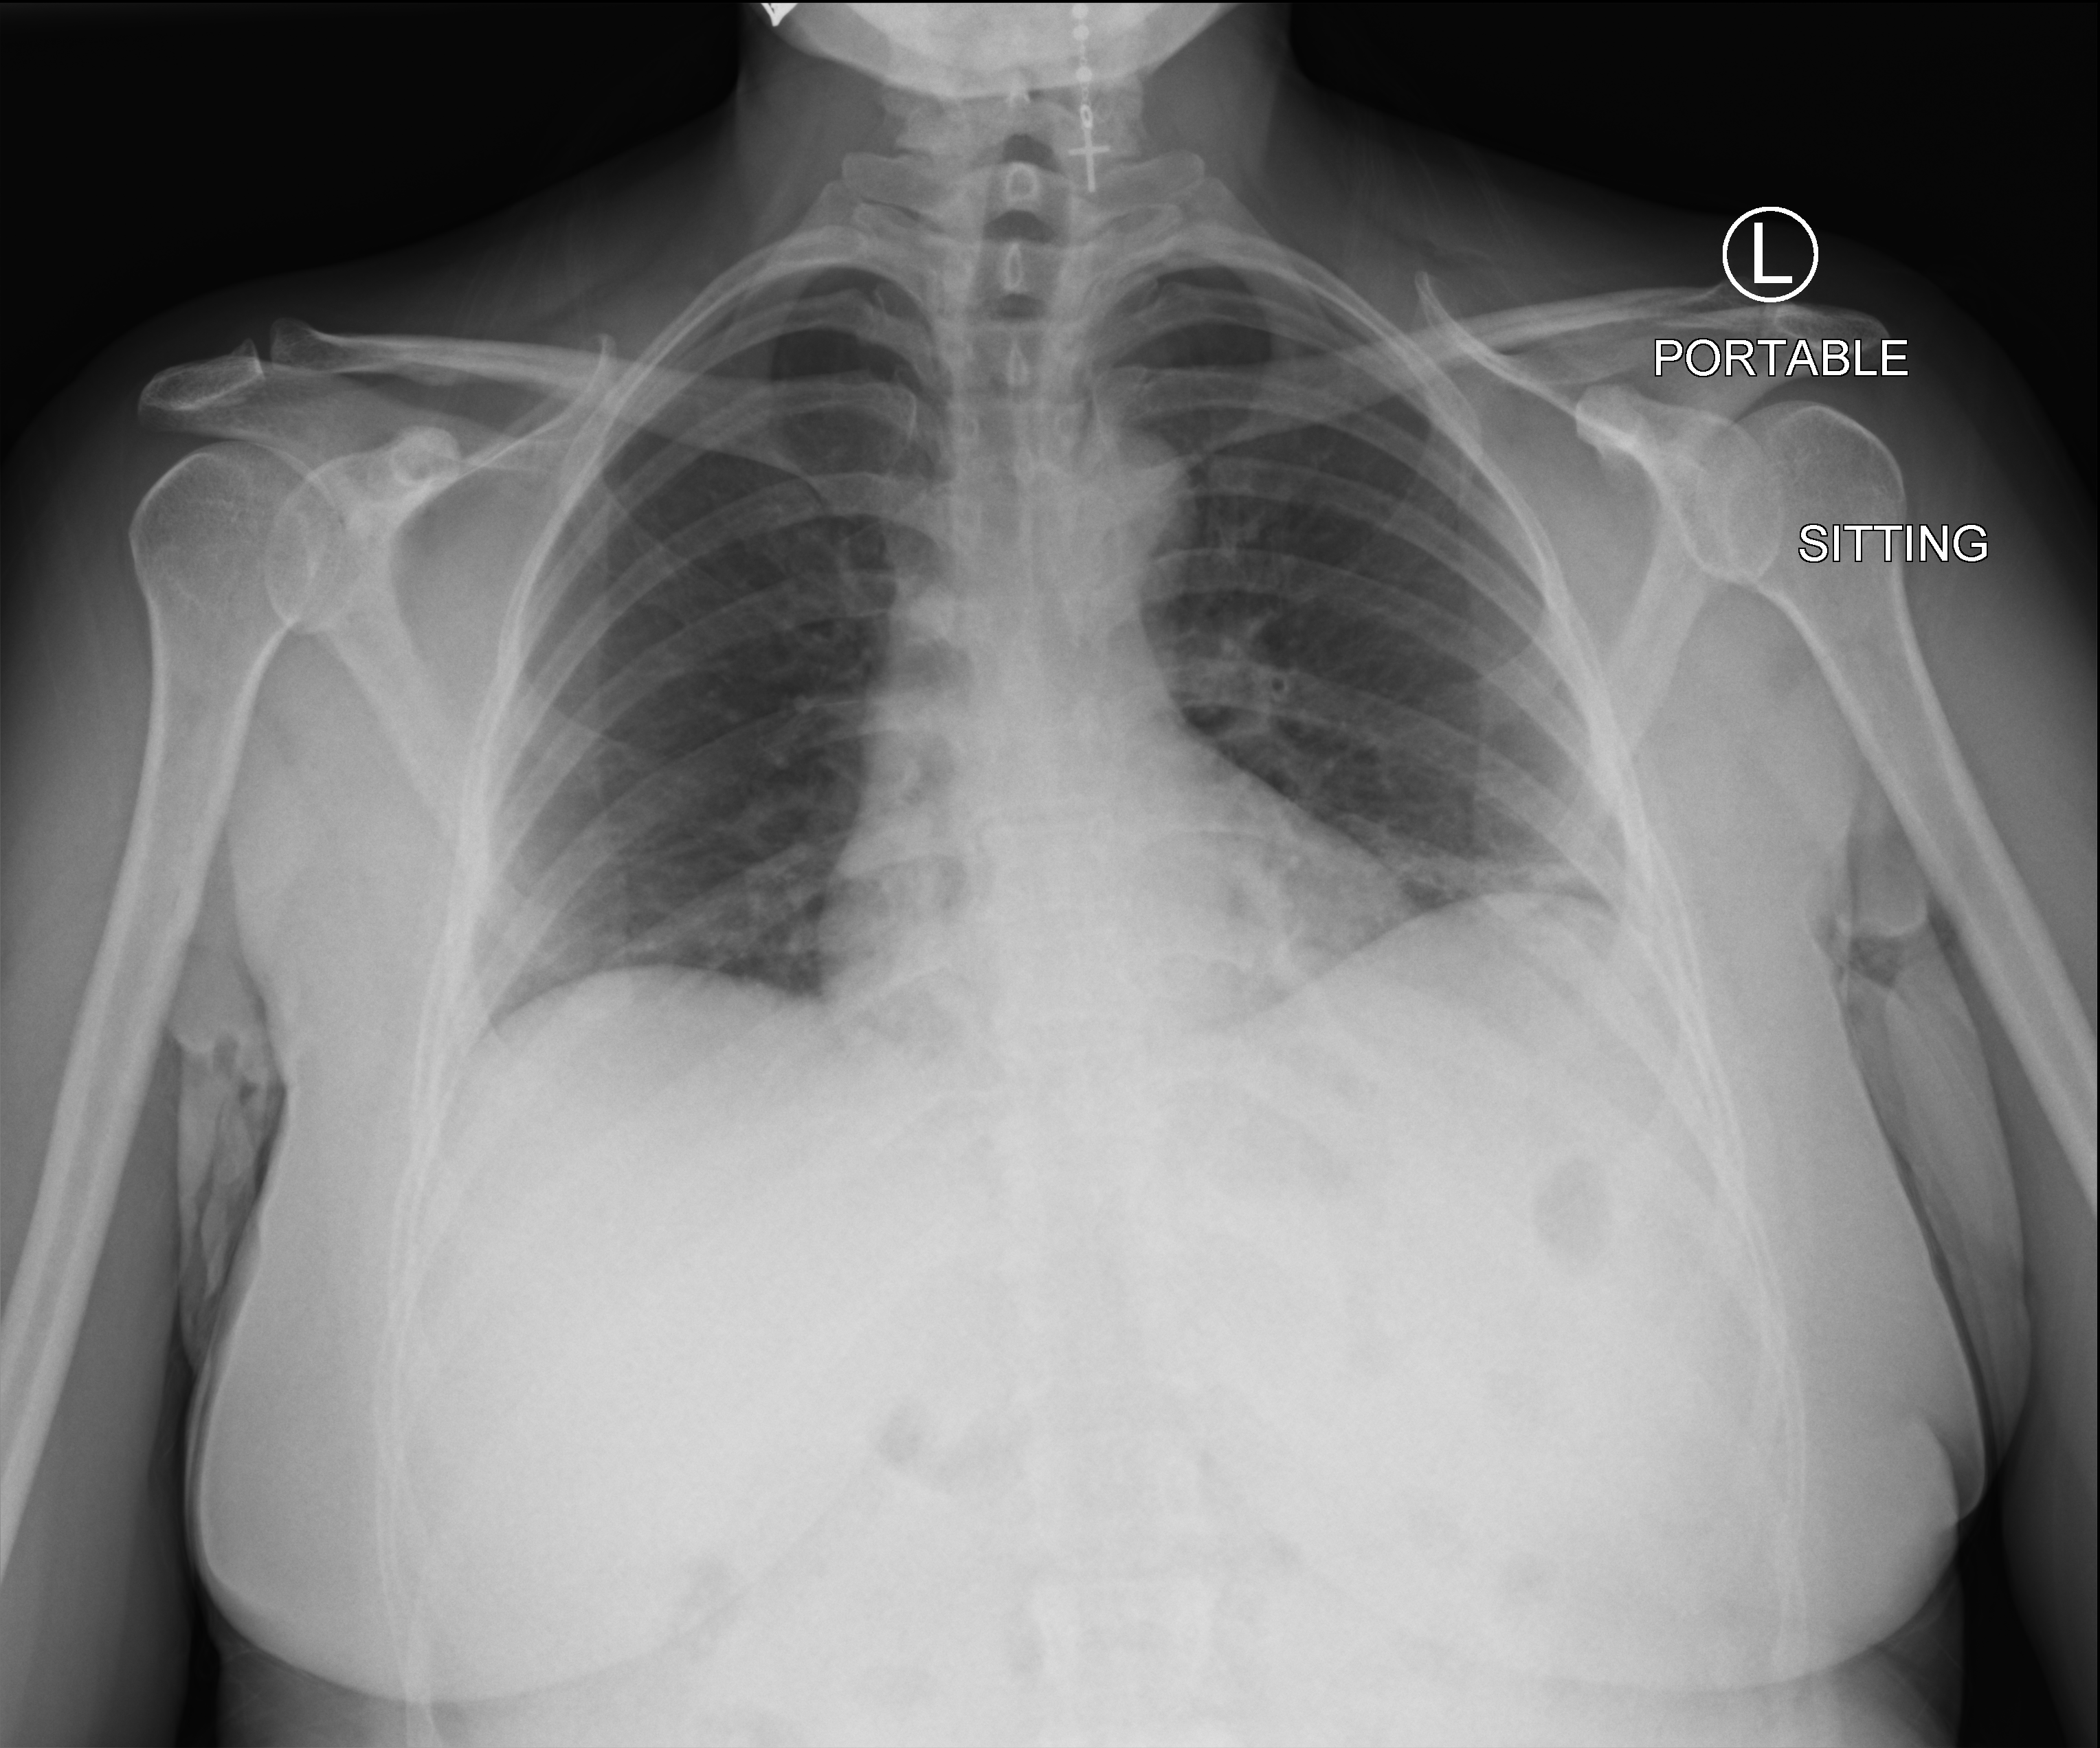
Portable chest radiograph, anteroposterior (AP) projection. Female patient hospitalised with COVID-19, age 18–59 years.
Admission-level facts for this patient (not findings on this image; timing relative to this image not recorded): diabetes (admission record): no; mechanically ventilated during this hospital stay: no; length of hospital stay: 1 day.